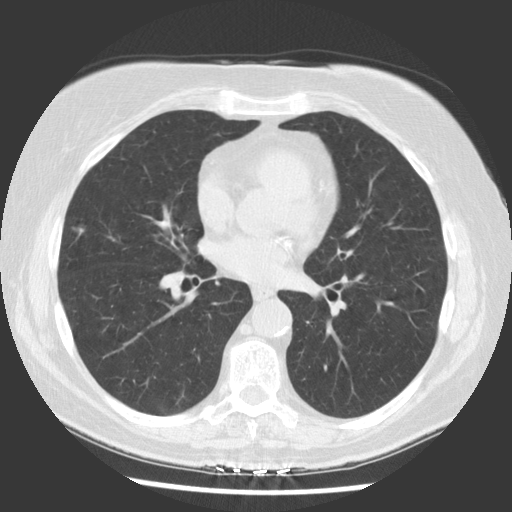
Low-dose screening chest CT, axial slice; first (baseline) screen; lung window (W 1500 / L -600 HU); standard (soft-tissue) reconstruction kernel (STANDARD); 140 kVp; slice 77 of 142 in the series. Female, age 66 years at enrolment. Current smoker at enrolment.
Expert reader's lesion annotation, bounding box <53,213,99,254> (left, top, right, bottom; pixels). The screening reader recorded 2 non-calcified nodules or masses ≥4 mm on this exam; which of them this box marks is not recorded. Official screen result: positive, change unspecified: nodule(s) >= 4 mm or enlarging nodule(s), mass(es), or other non-specific abnormalities suspicious for lung cancer. Participant outcome: lung cancer diagnosed 68 days after this screen — bronchiolo-alveolar carcinoma, mucinous, right middle lobe, well differentiated (G1), stage IA (AJCC 6th edition), 9 mm at pathology.